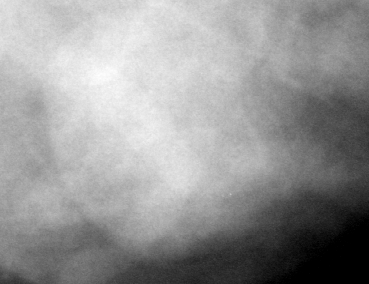
Crop from a digitized film mammogram around one marked abnormality, left breast, MLO view, BI-RADS breast density category 3 (scale 1–4).
- Marked abnormality: mass, shape oval, margins circumscribed; BI-RADS assessment category 3; pathology result (as recorded, not read from the image): benign.